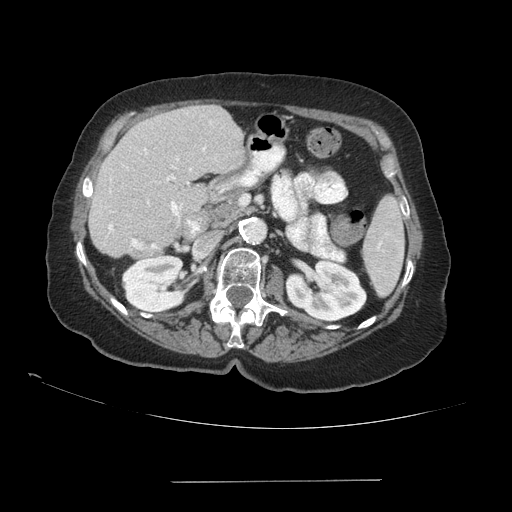
Contrast-enhanced abdominal CT (liver protocol), one axial slice; position 45 of 89 along the scan axis; reconstruction kernel STANDARD; soft-tissue window (W 400 / L 40 HU); 2.5 mm slice thickness; 512 × 512 image matrix. From the clinical record (not read from this slice): diagnosis: hepatocellular carcinoma (patient treated with transarterial chemoembolisation; whether this scan precedes or follows treatment is not stated here); TNM stage (as recorded): Stage-IVA; Child-Pugh class: A; tumour differentiation: poorly differentiated.
Annotated regions visible in this slice (semi-automatically segmented with operator editing):
- liver parenchyma outside the tumour (the mass and vessels are separate outlines, so this box may not span the whole liver): bounding box <88,104,244,256> (left, top, right, bottom; pixels)
- liver vessels: <108,147,206,249>